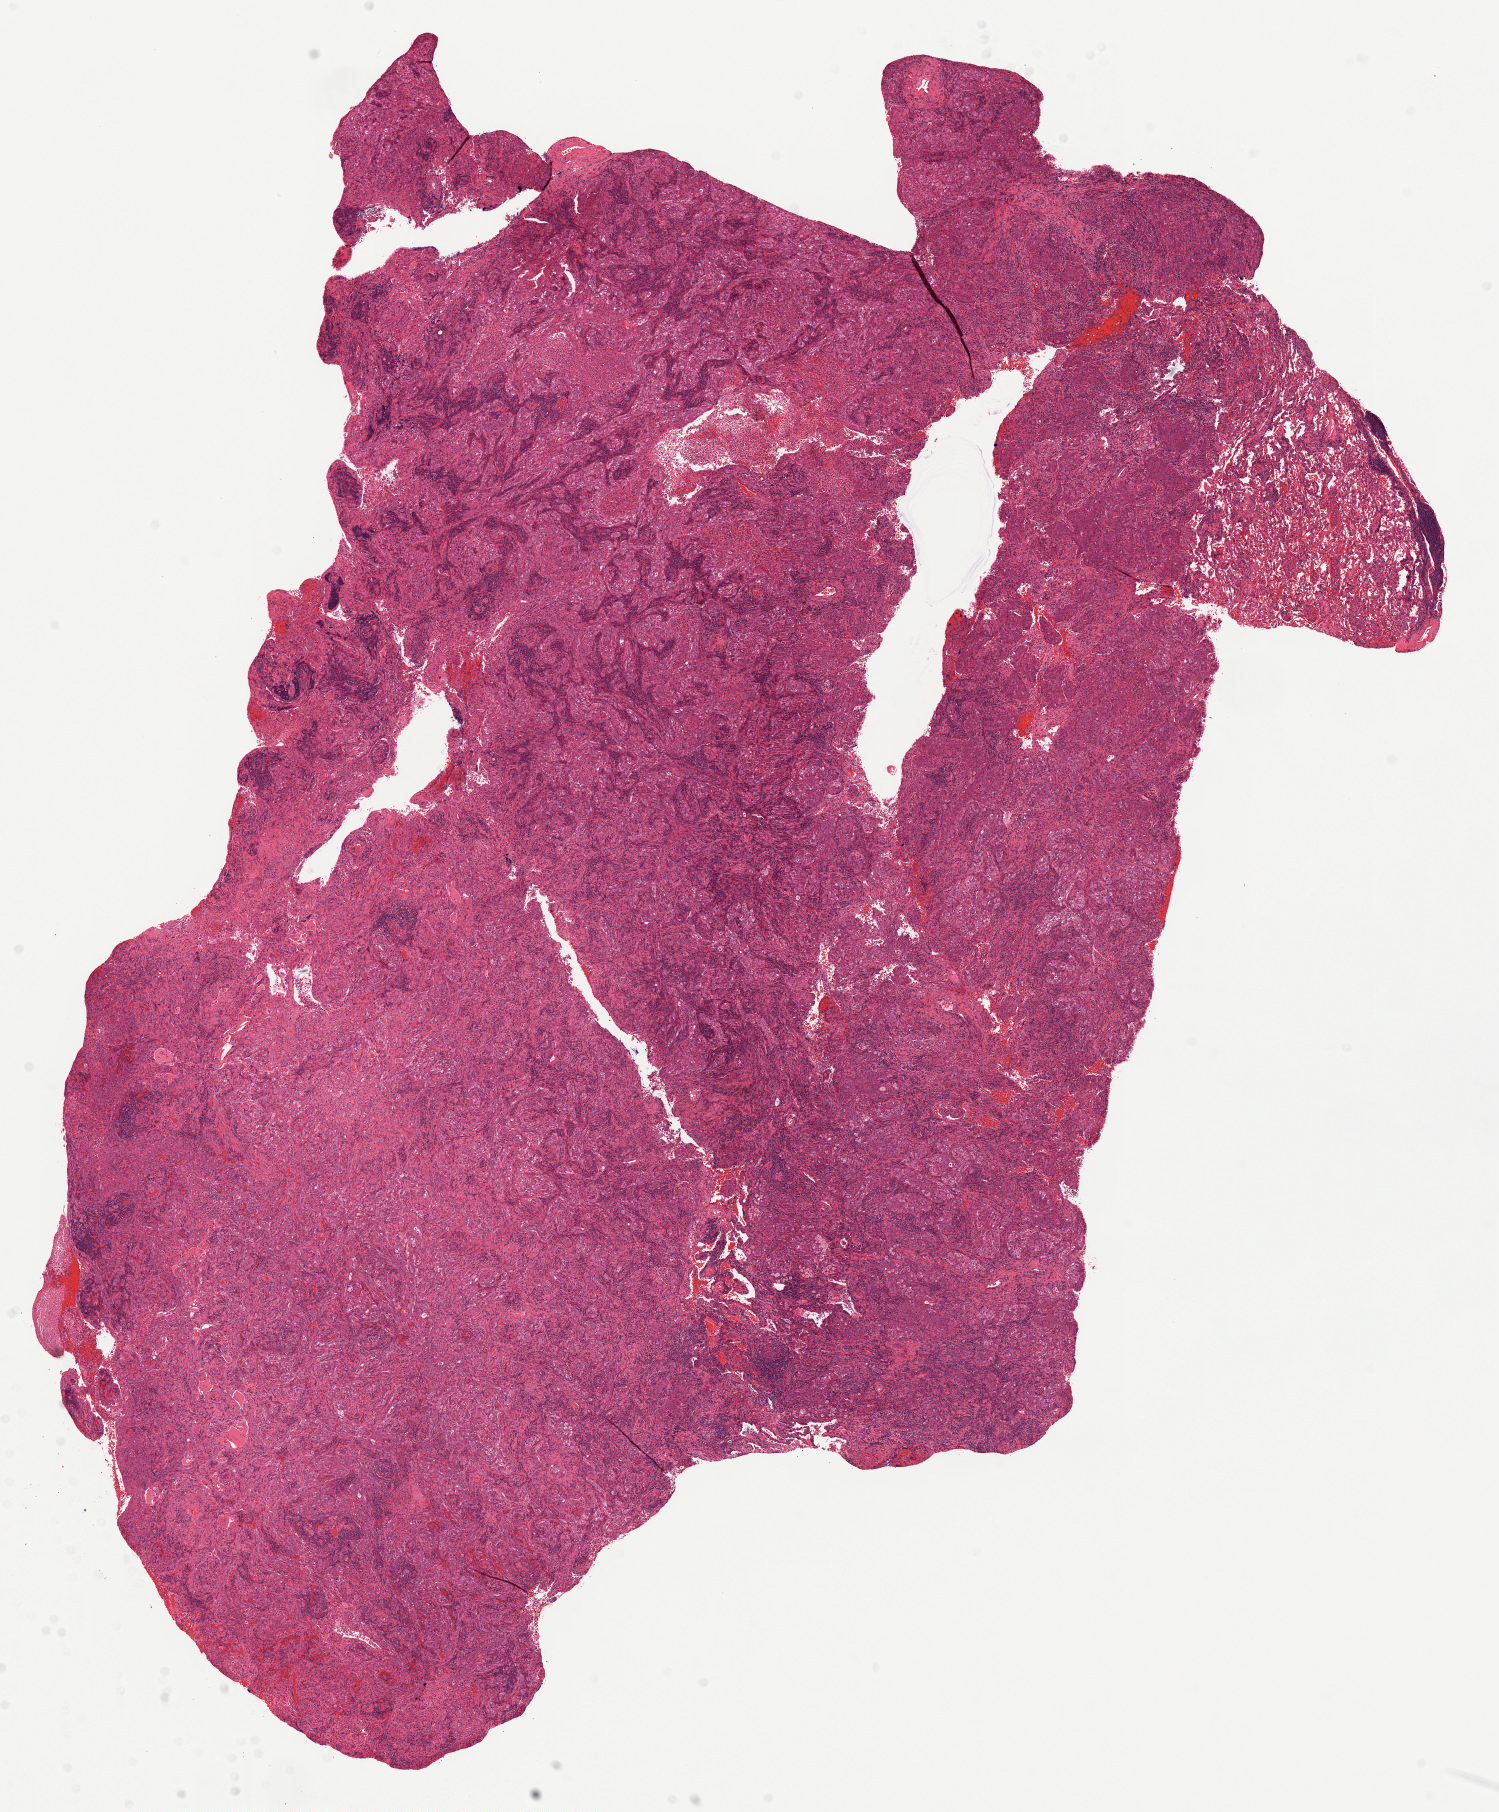
Digitized Hematoxylin and eosin (H&E) stained tissue section (whole slide), whole scanned area (about 12.0 x 14.5 mm, acquisition: 20x scan) shown as a low-resolution overview; formalin-fixed paraffin-embedded (FFPE) diagnostic section; sample: primary tumour, lung. Patient: female, age at initial diagnosis 78 years.
• AJCC pathologic stage: IIB (6th edition)
• histologic diagnosis: Squamous cell carcinoma, NOS (upper lobe, lung)
• TNM: T3 N0 M0